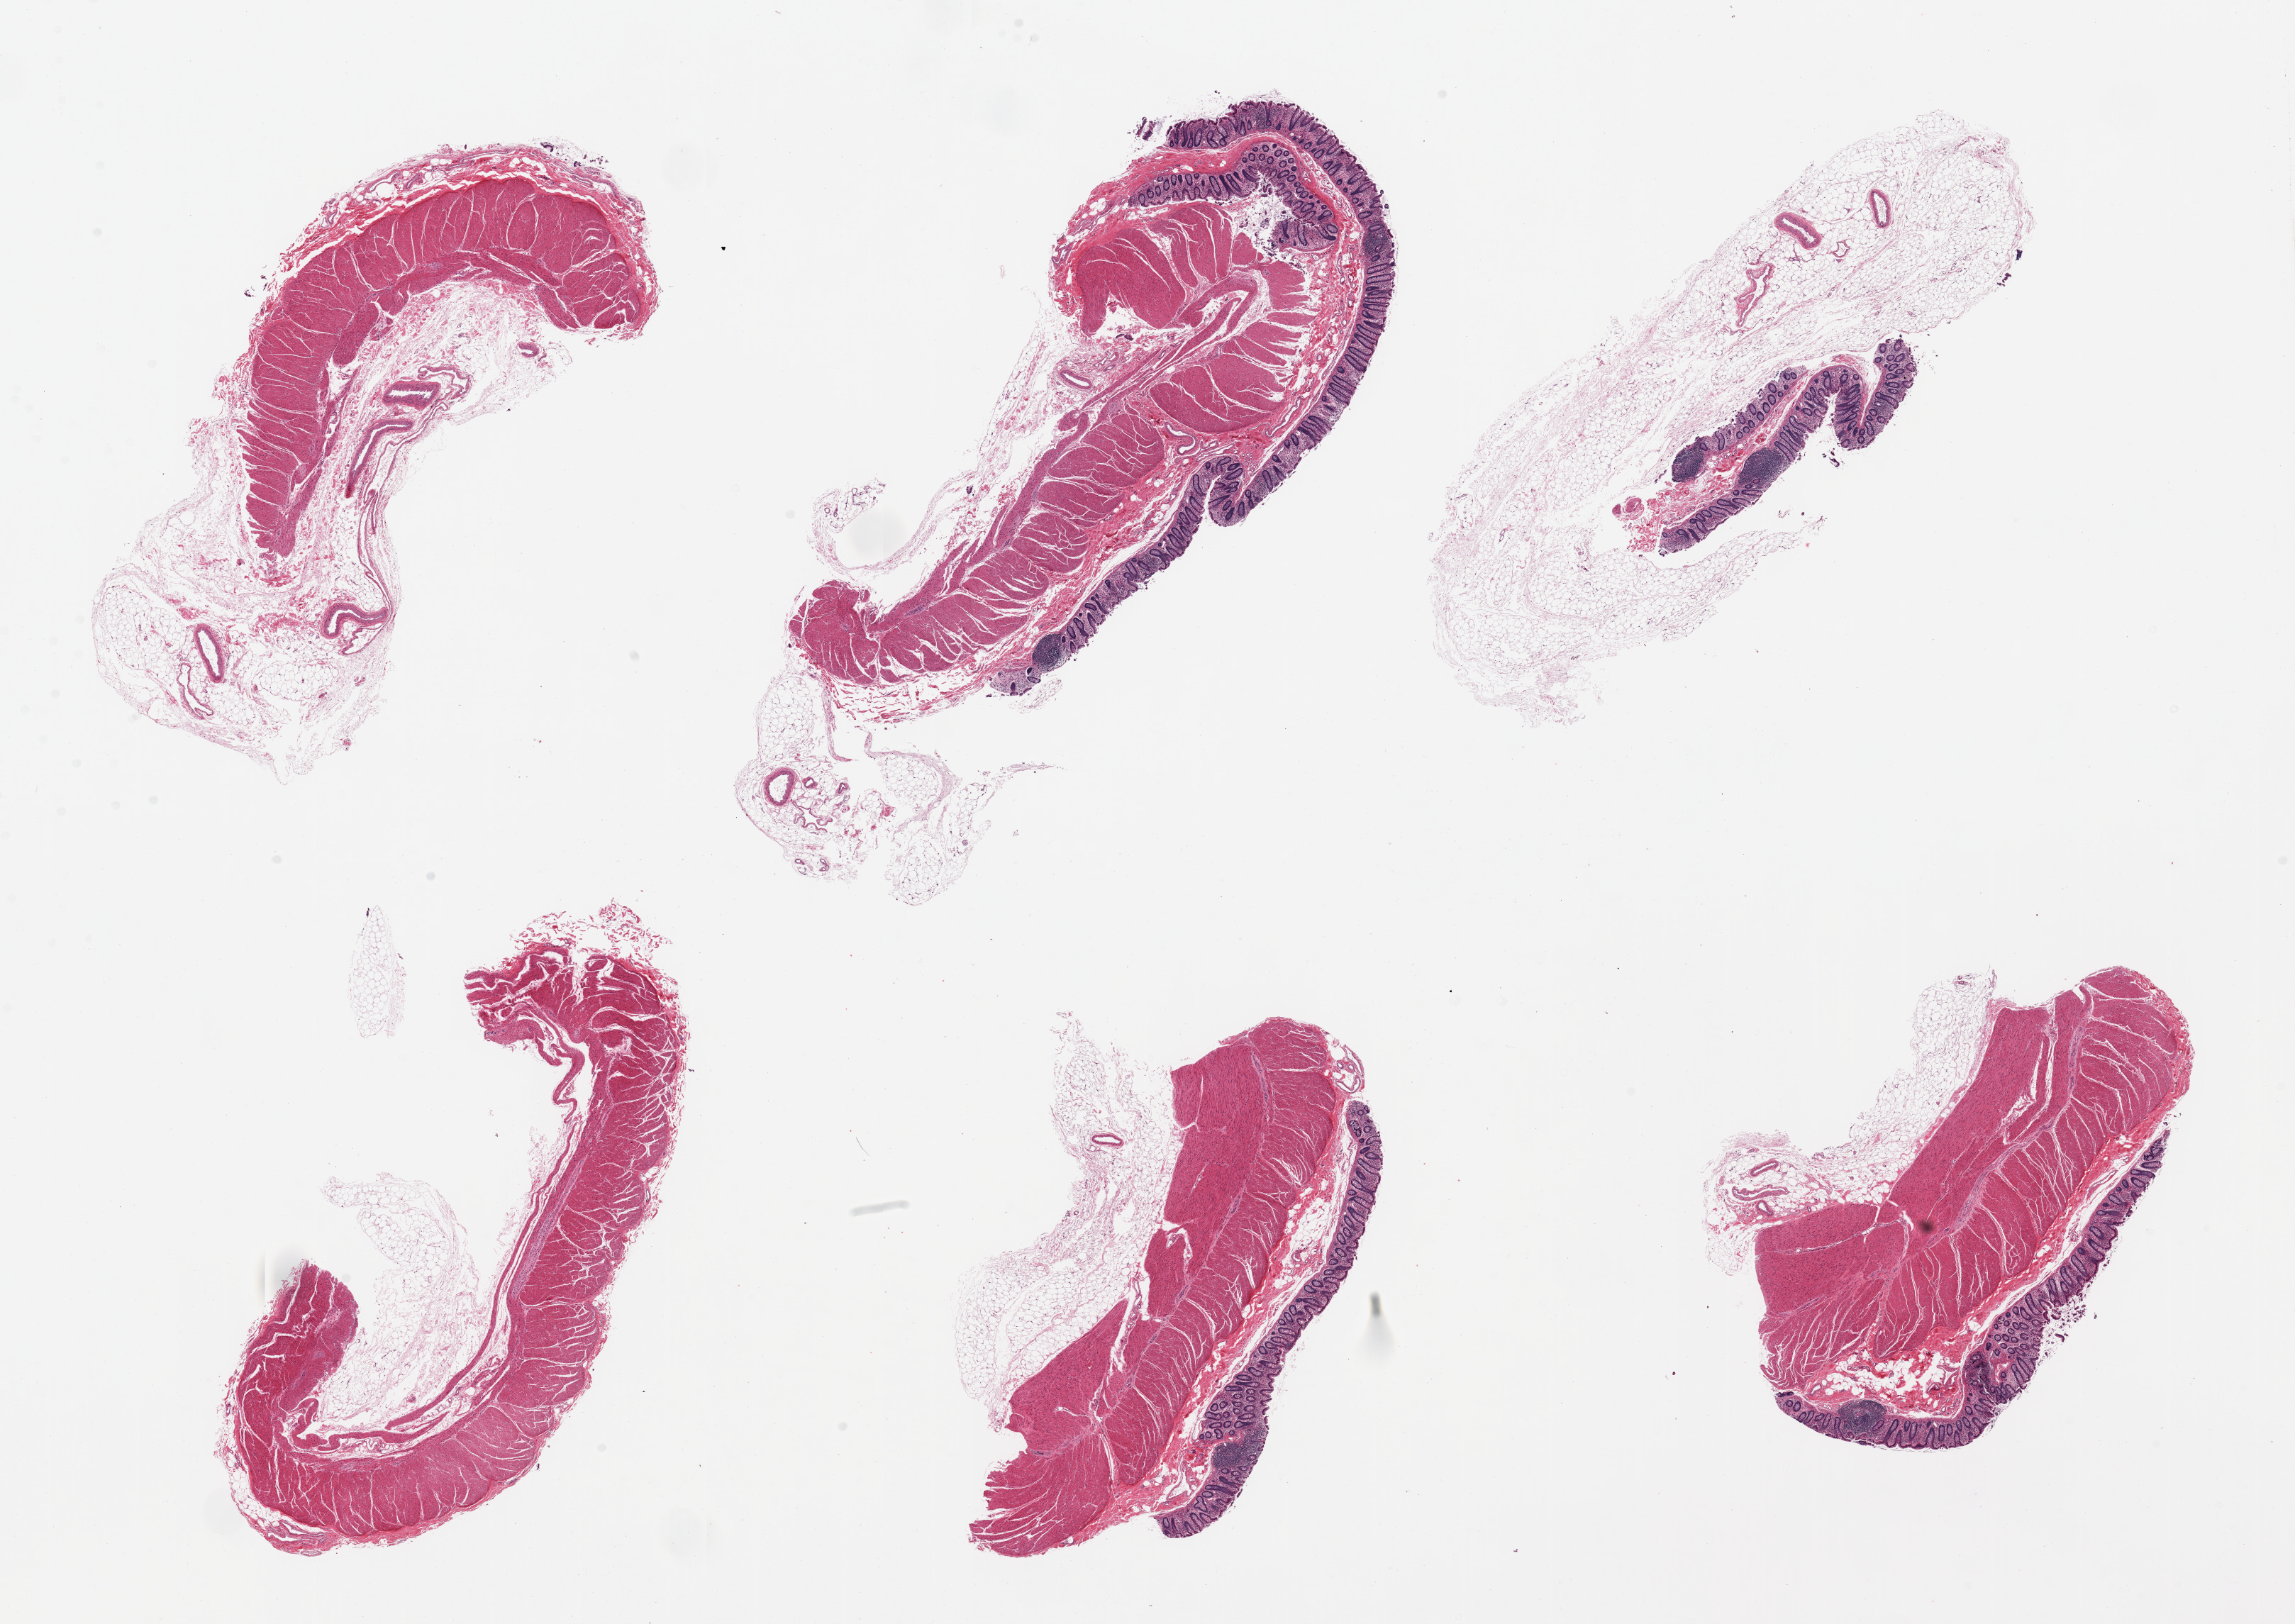
Whole-slide image, H&E stain, shown as a low-resolution overview of the whole scanned area (about 25.6 x 18.1 mm, slide scanned at 20x). PAXgene-fixed paraffin-embedded (PFPE) section. Section of transverse colon (target tissue). Tissue donor sample. Male donor.
Pathologist's review note for this sample: 6 pieces, mucosa up to ~0.4mm.